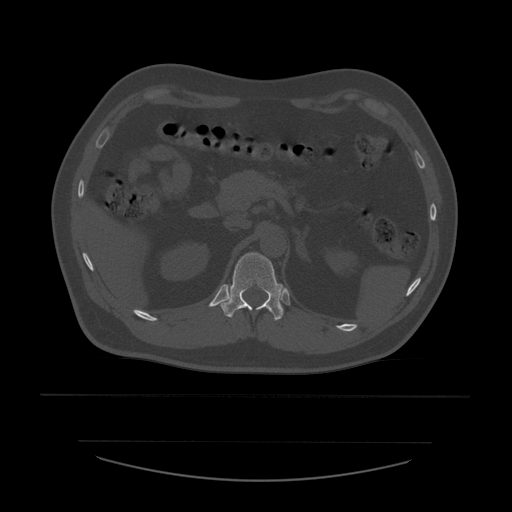
CT including the spine, one axial slice; position 253 of 532 along the scan axis; reconstruction kernel STANDARD; bone window (W 1800 / L 400 HU); 1.25 mm slice thickness; 512 × 512 image matrix, field of view 441 × 441 mm. Patient age 44 years. Case-level facts recorded for this patient, not image findings: primary cancer: soft tissue sarcoma.
Annotated regions visible in this slice (semi-automatically segmented with operator editing):
- T12 vertebra: bounding box (x1, y1, x2, y2) in pixels: (221, 253, 284, 321)